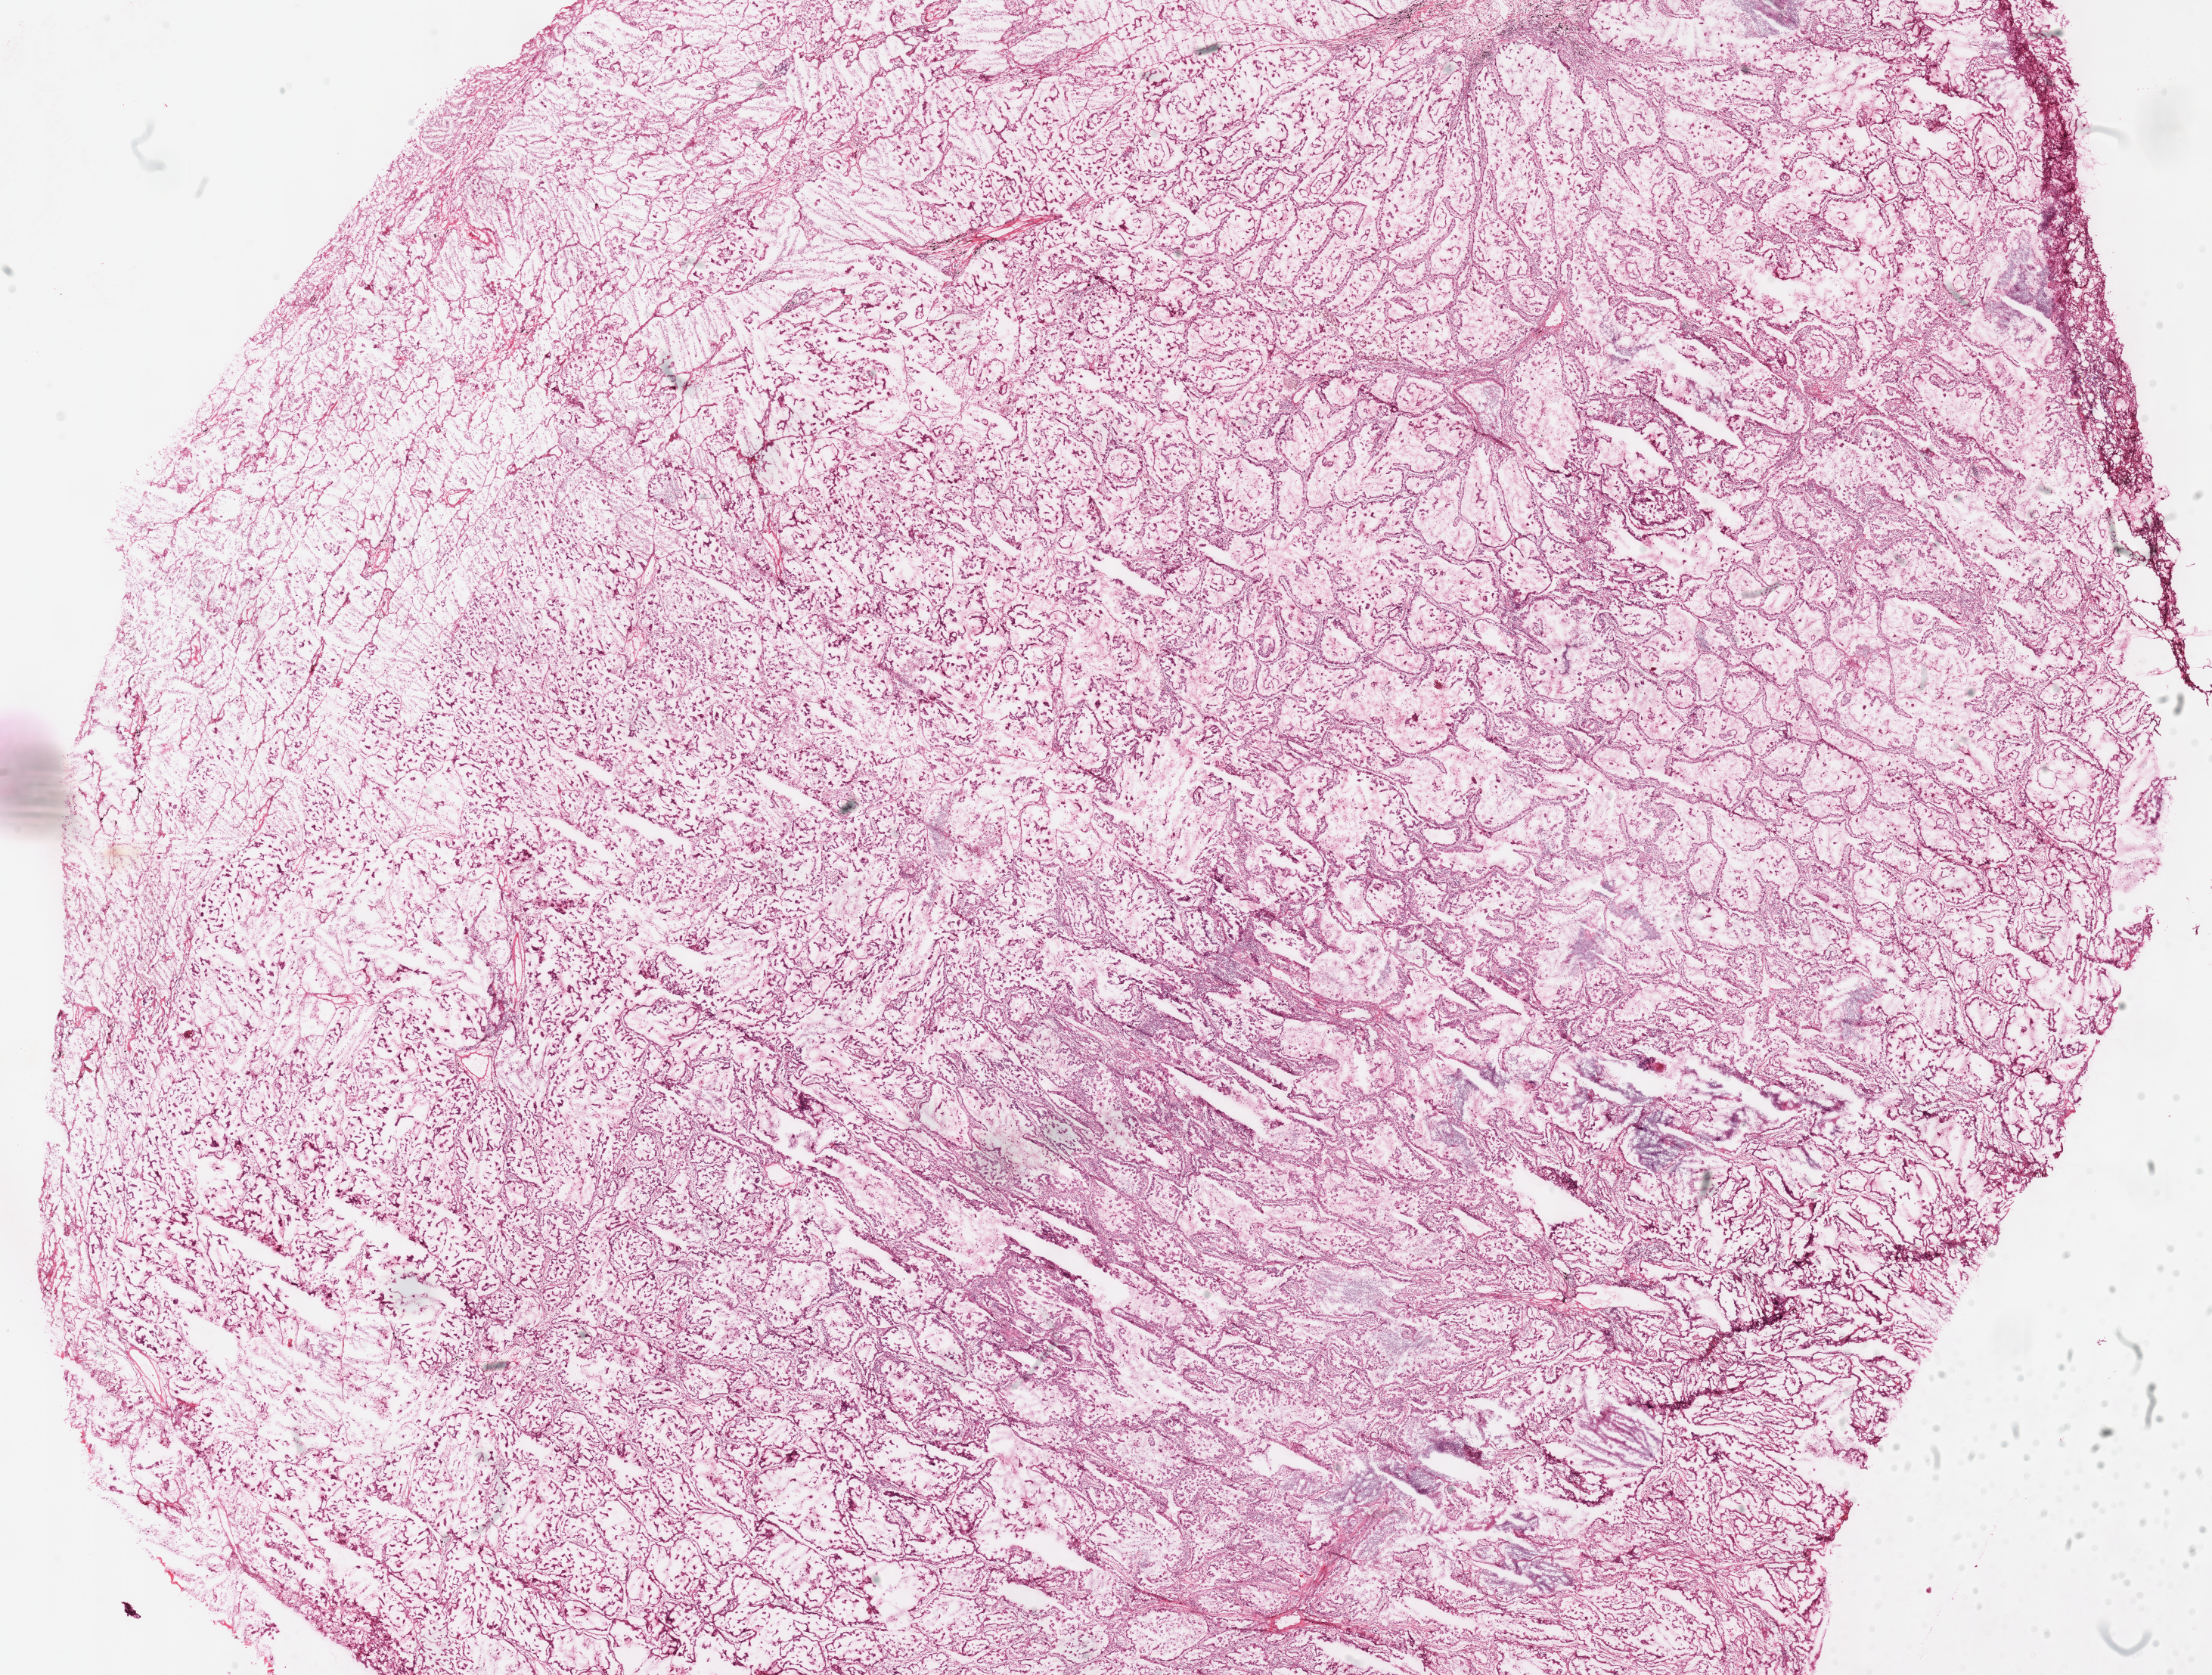
Whole-slide histology image, H&E-stained — whole scanned area (about 23.0 x 17.4 mm) shown as a low-resolution overview; frozen section from the top of the tissue portion; primary tumour sample from the lung. Male, age 52 years at initial diagnosis. Pathologist review of this section (percent, as recorded): tumour cells 85%, tumour nuclei 70%, normal cells 0%, stromal cells 15%, necrosis 0%.
* laterality: left
* histologic diagnosis: Adenocarcinoma, NOS
* AJCC pathologic stage: IIIA (7th edition)